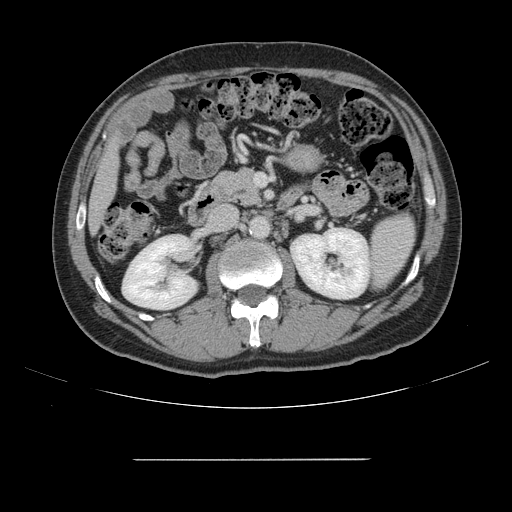
Contrast-enhanced abdominal CT, one axial slice; slice 59 of 164 in the series (ordered by position); intravenous contrast given; soft-tissue window (W 400 / L 40 HU); 2.5 mm slice thickness; 512 × 512 image matrix, field of view 404 × 404 mm. Male patient, age 54 years. Case-level facts recorded for this patient, not image findings: diagnosis: colorectal cancer liver metastases, imaged before liver resection; multiple liver metastases: yes; largest metastasis: 1 cm; disease in both lobes: no.
Structures marked on this image (manually delineated by an expert):
- liver: bounding box (x1, y1, x2, y2) in pixels: (90, 147, 117, 228)
- planned liver remnant (the part of the liver to remain after resection): (90, 147, 117, 228)